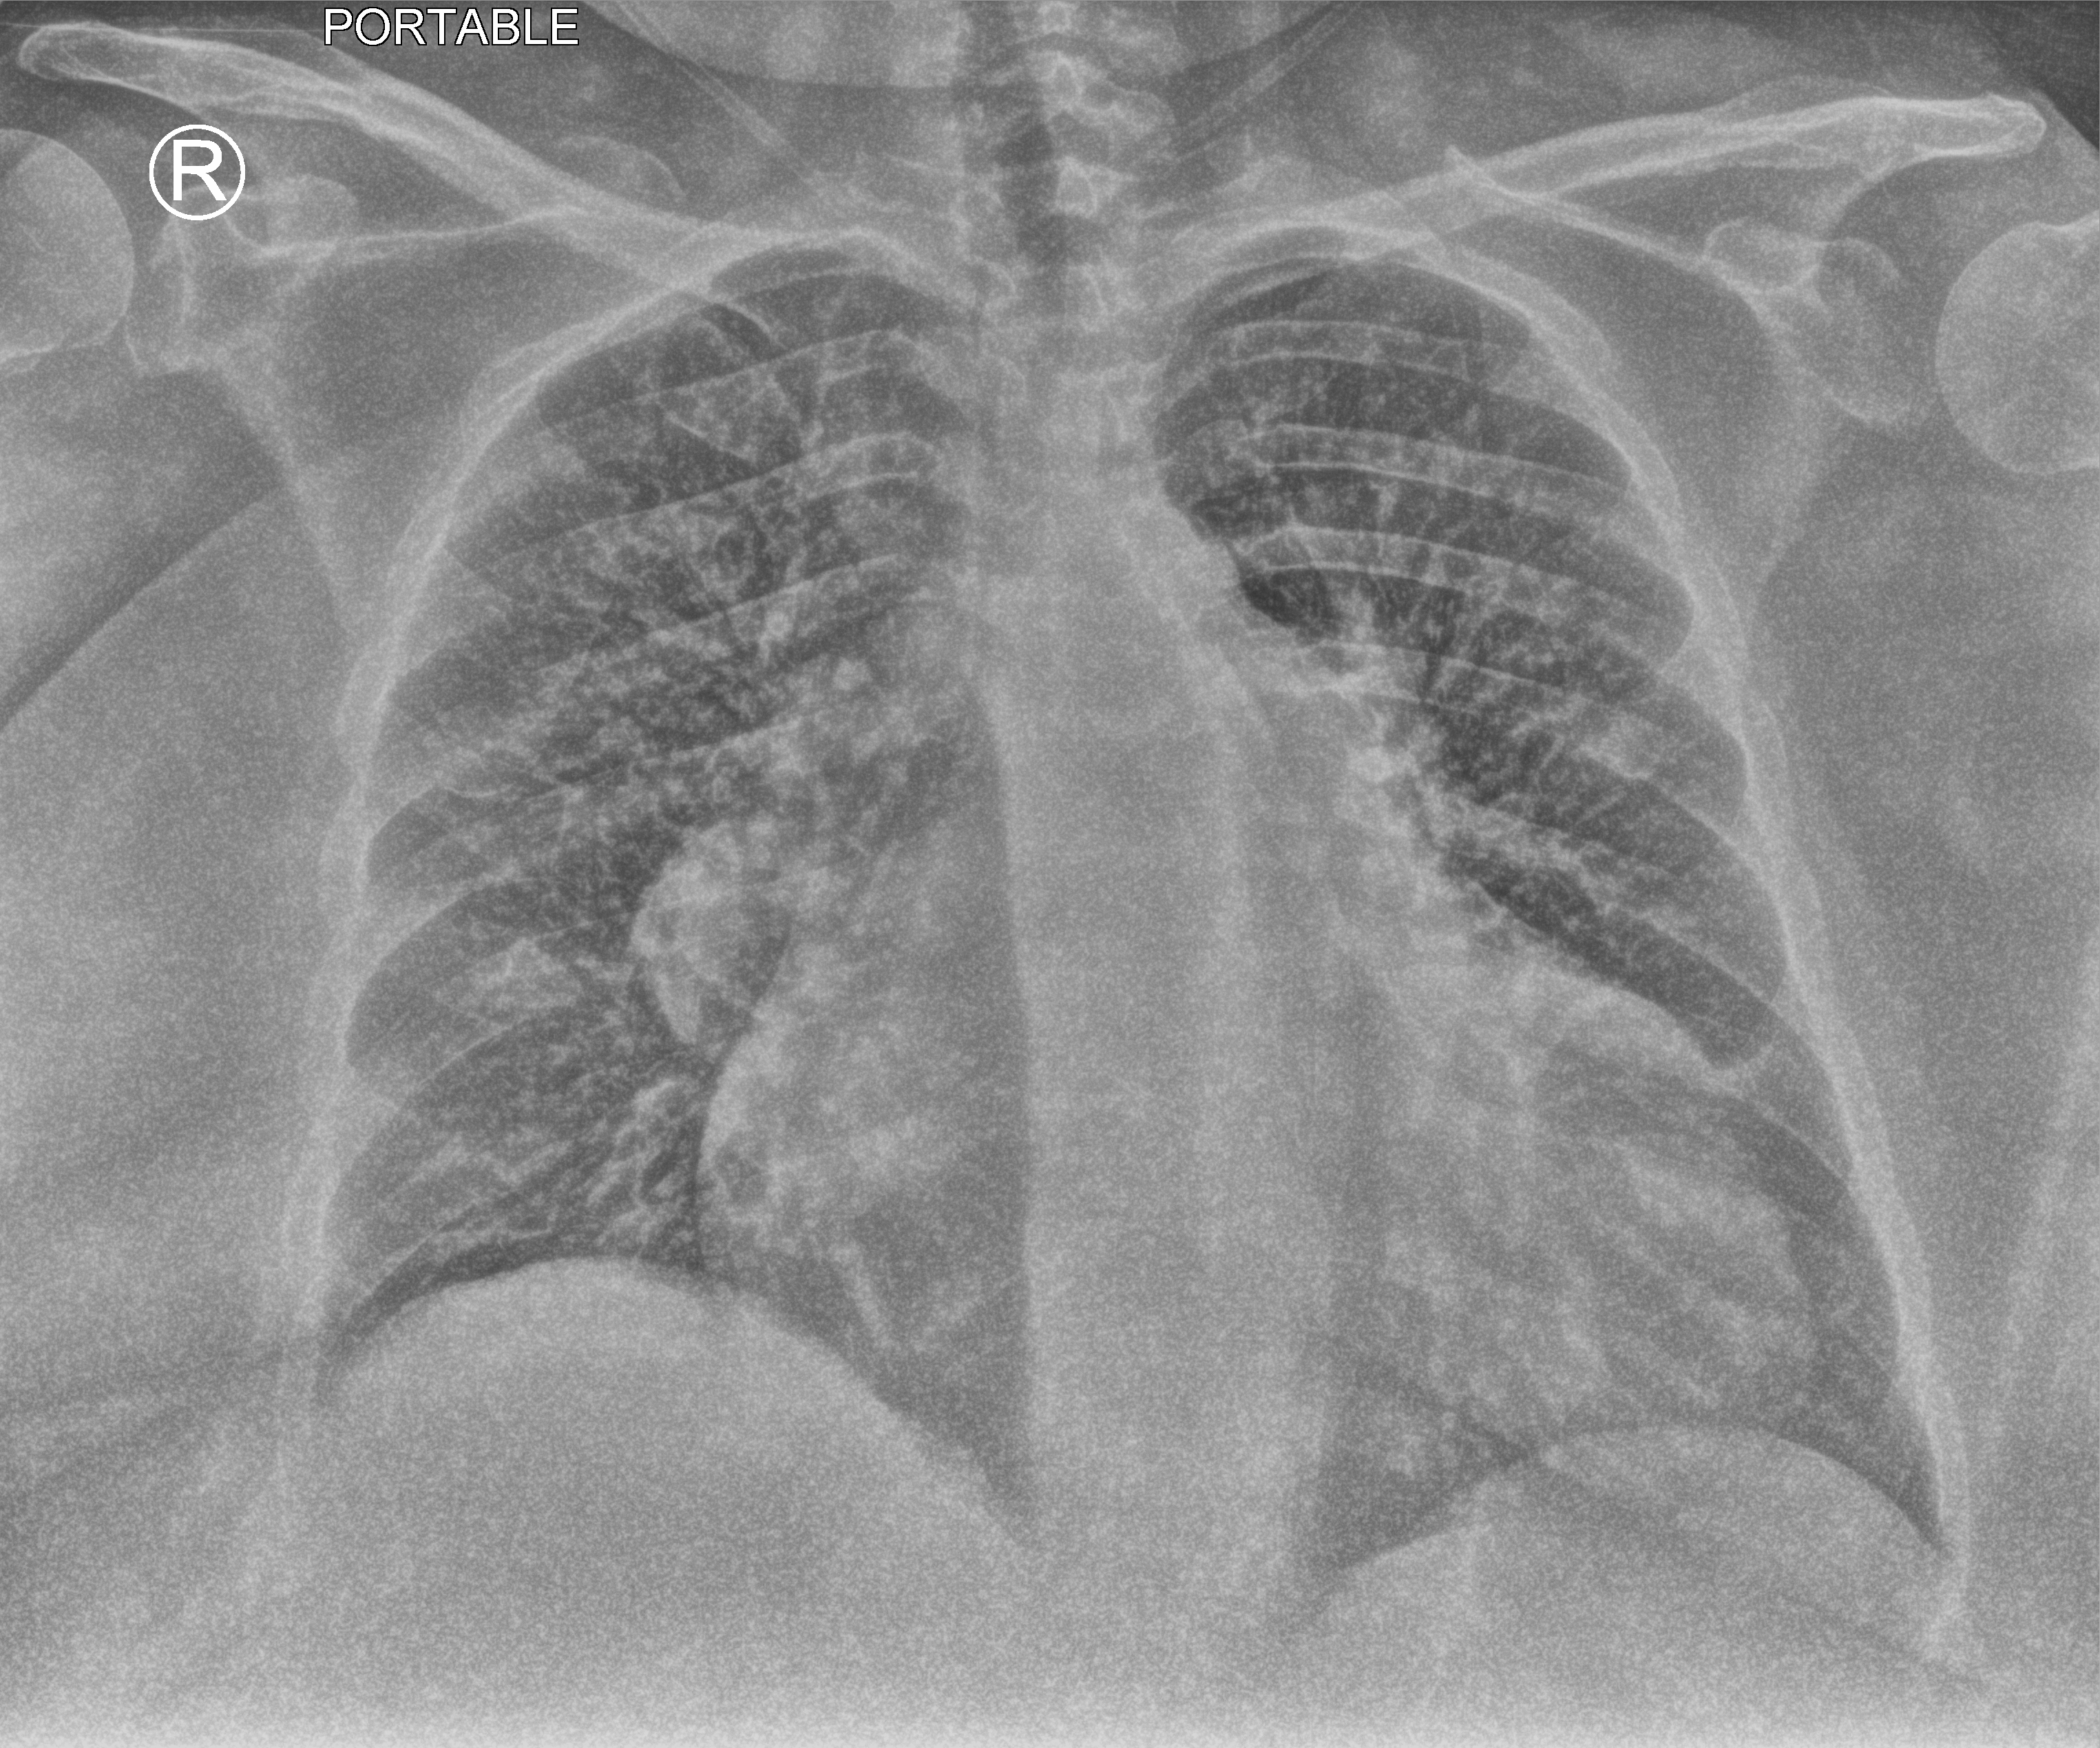
Bedside chest radiograph (computed radiography); anteroposterior (AP) projection. Patient hospitalised with COVID-19; female, aged 60–74 years.
From the hospital-stay record, not from the radiograph (when in the stay this image was taken is not recorded): admitted to intensive care during this hospital stay: yes; length of hospital stay: 6 days.